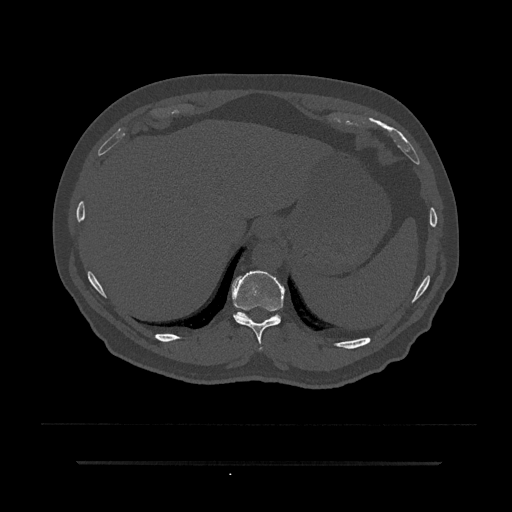
CT including the spine, one axial slice; position 313 of 797 along the scan axis; 120 kVp; bone window (W 1800 / L 400 HU); 0.5 mm slice thickness; 512 × 512 image matrix, field of view 464 × 464 mm. Male patient, age 59 years. Case-level facts recorded for this patient, not image findings: primary cancer: bile ducts; vertebrae with lytic lesions (as recorded): T10.
Annotated regions visible in this slice (semi-automatic segmentation, software-assisted and operator-edited):
- T10 vertebra: bounding box [x1, y1, x2, y2] px = [232, 271, 285, 350]
- T11 vertebra: [235, 312, 280, 320]